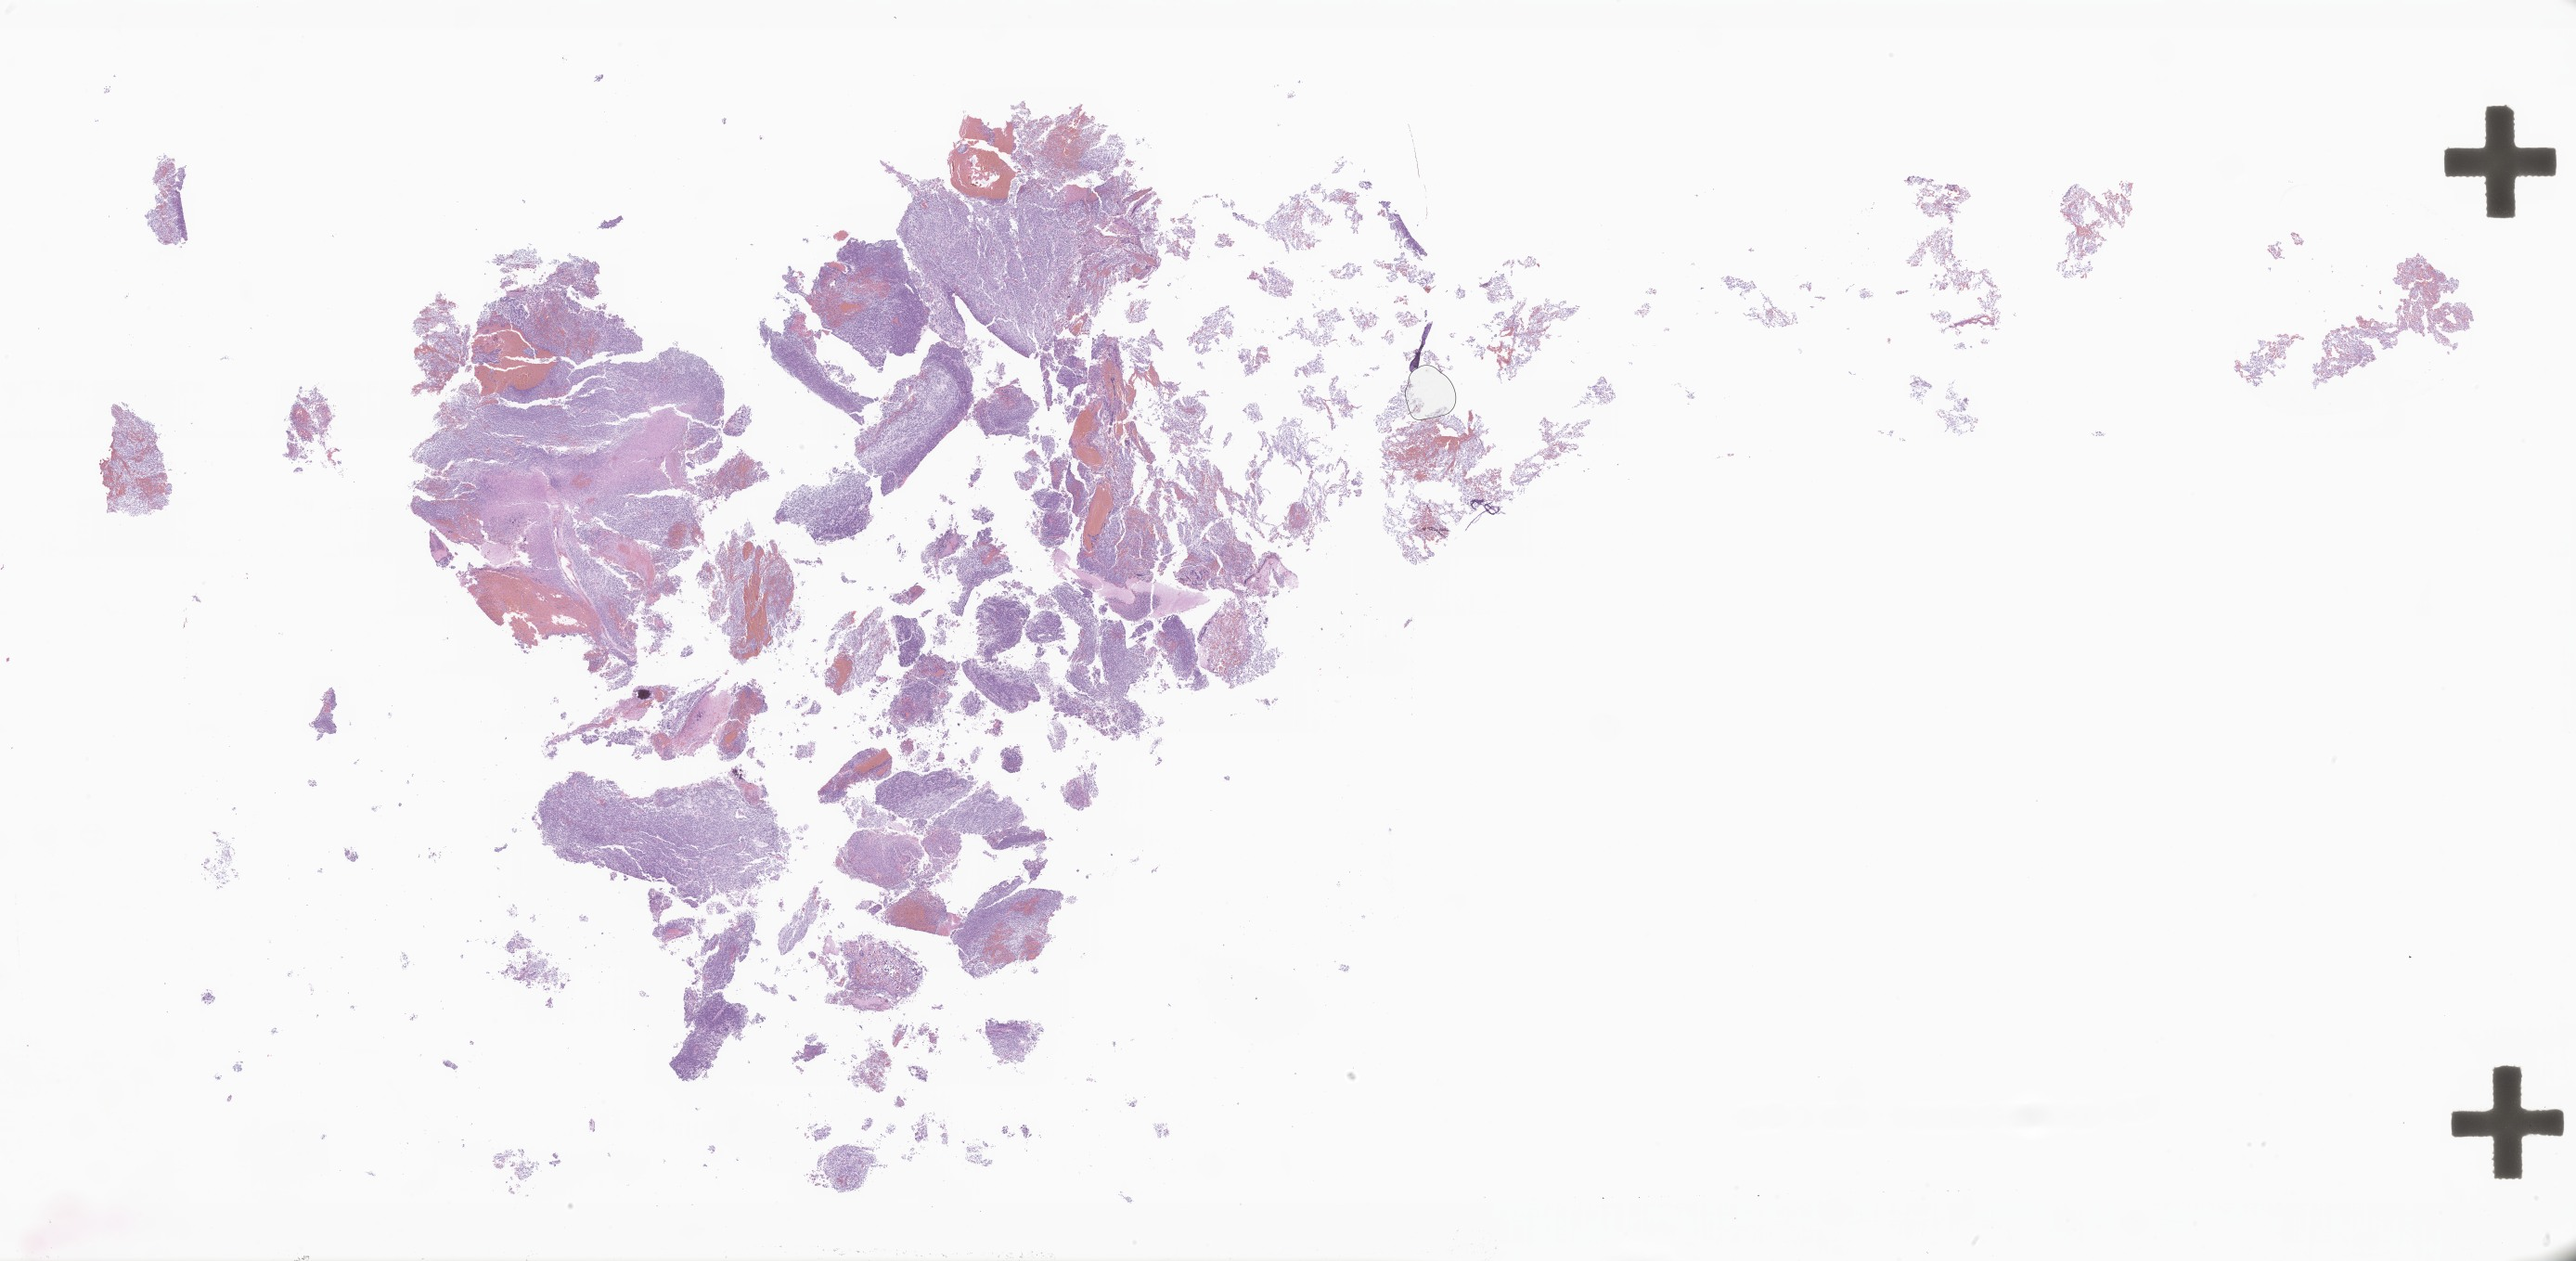
Hematoxylin and eosin (H&E) whole-slide image of tumor tissue from the brain, whole scanned area (about 46.8 x 22.9 mm) shown as a low-resolution overview. FFPE section. Patient female; age 116 months (9 years 8 months).
Recorded diagnosis: Neoplasm, malignant.